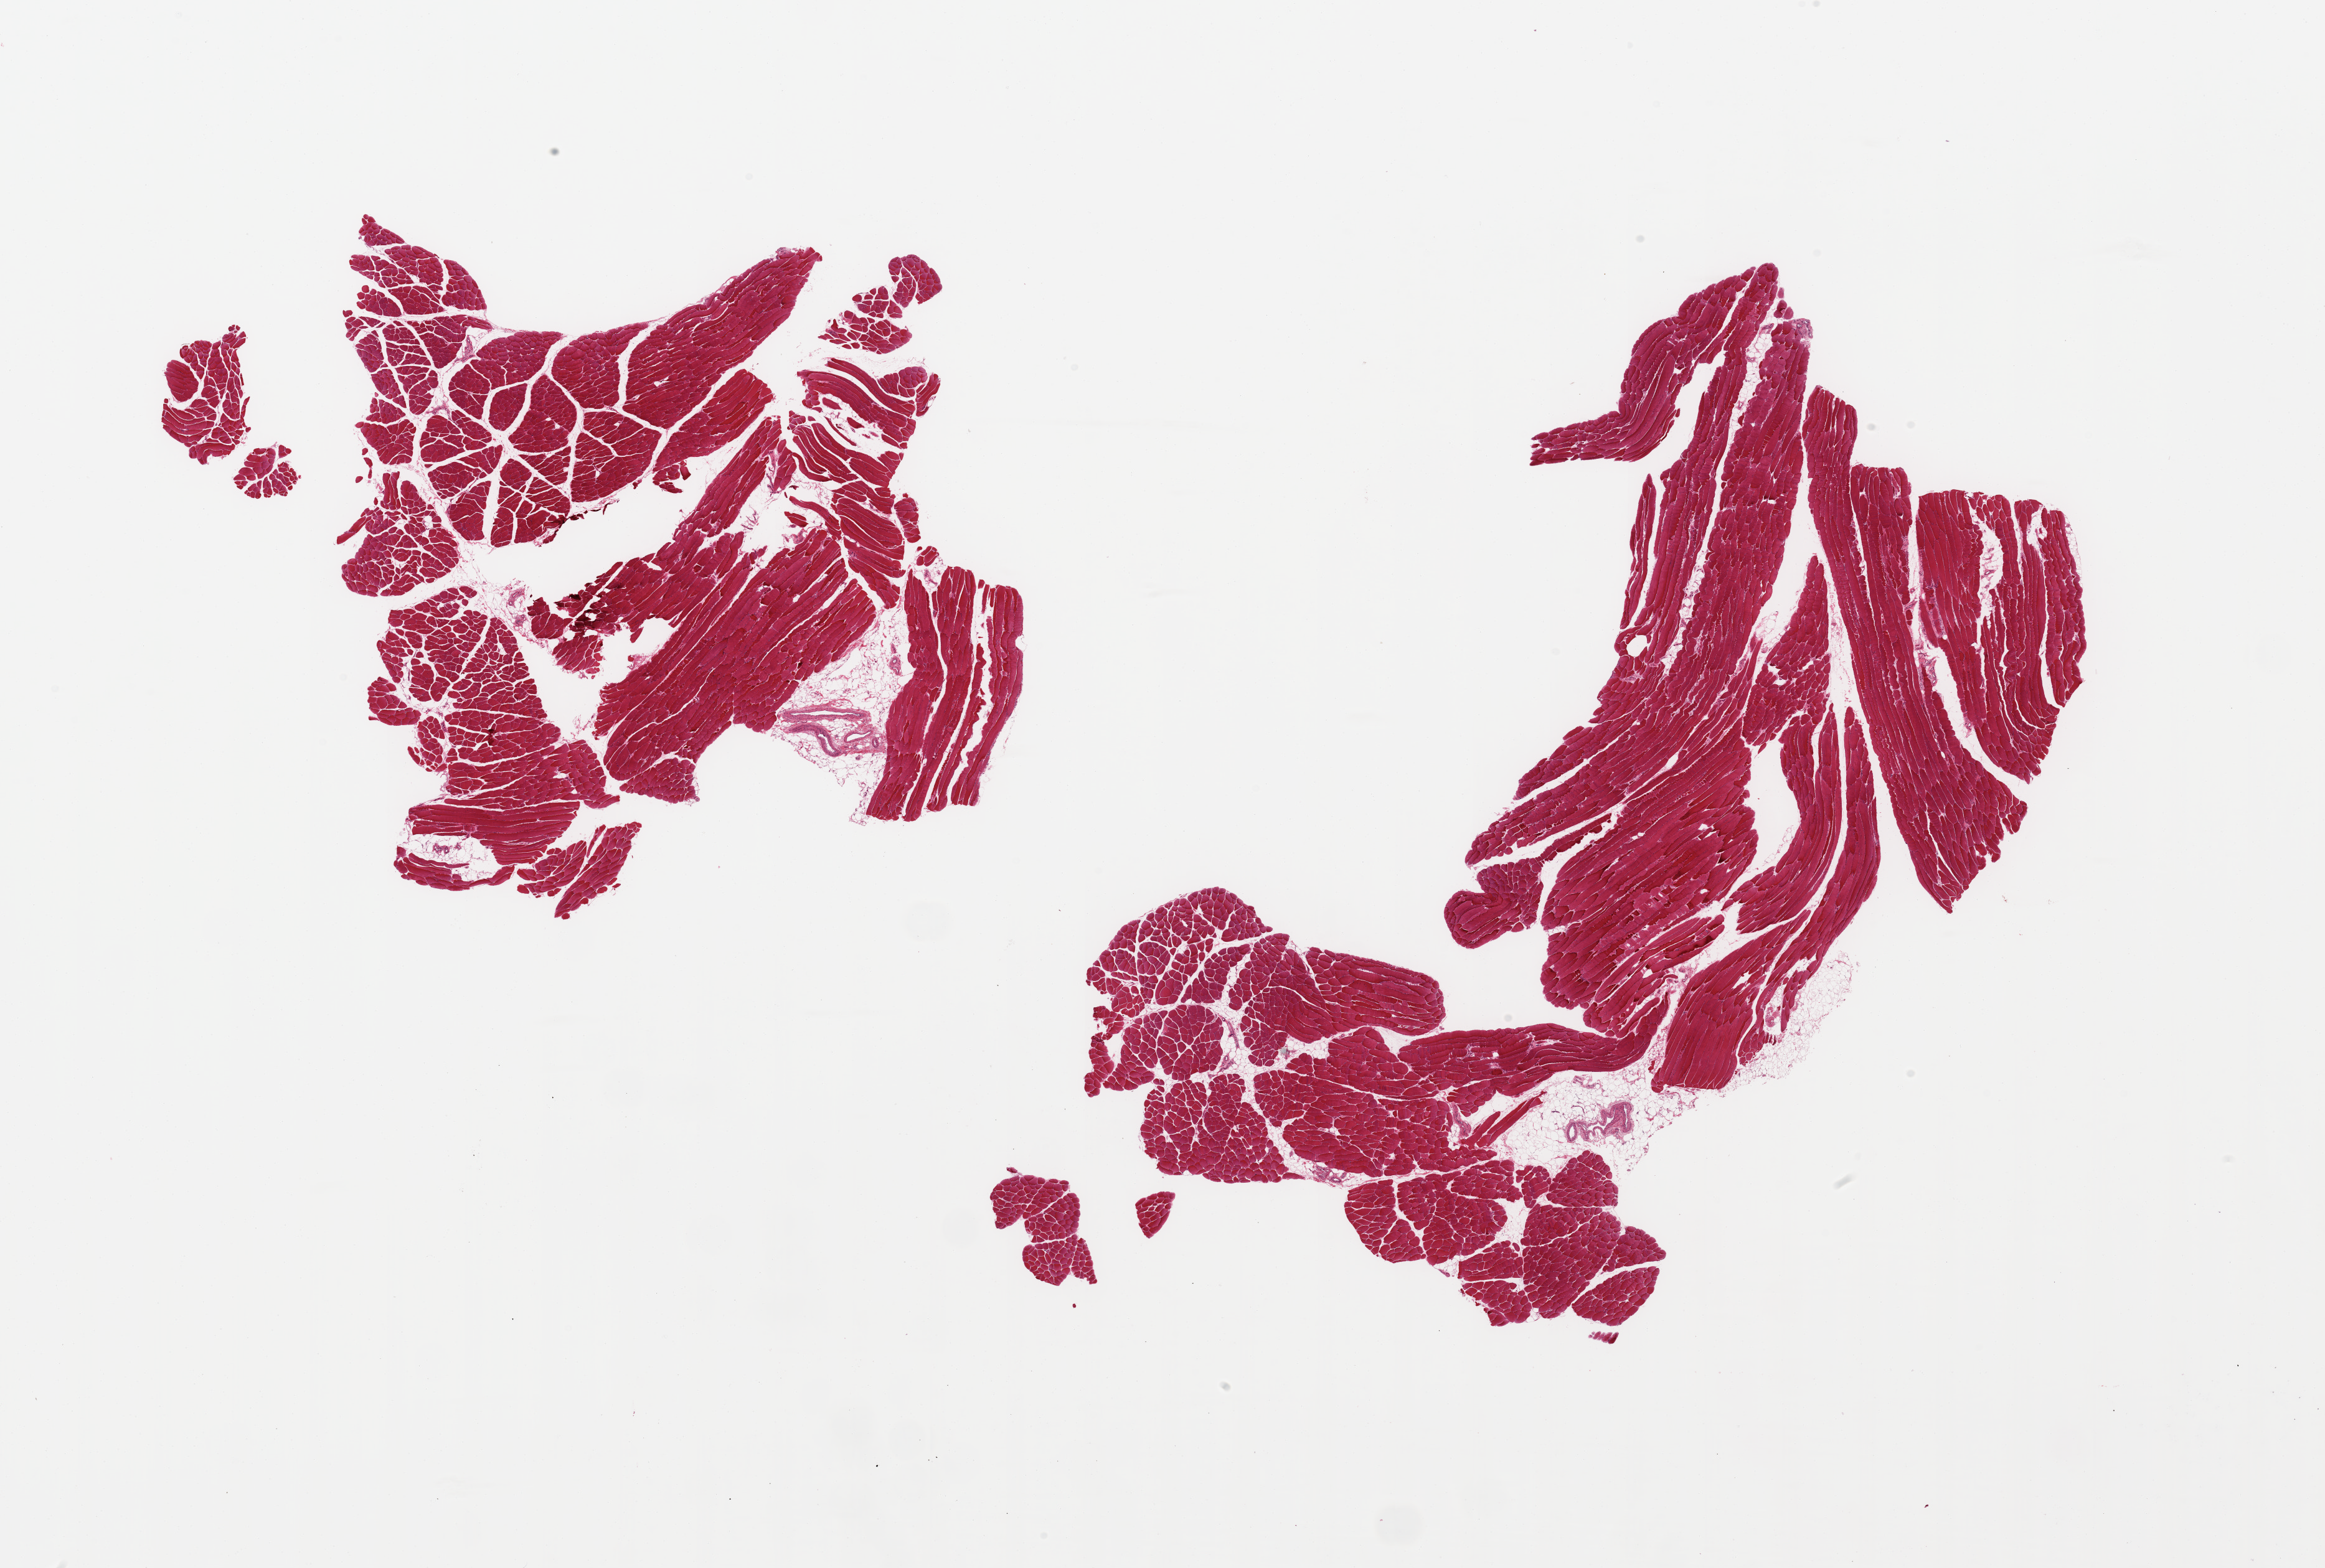
Digitized hematoxylin and eosin (H&E)-stained section, brightfield — low-resolution overview of the scanned area, about 29.5 x 19.9 mm, PAXgene-fixed paraffin-embedded (PFPE) section, target tissue: skeletal muscle, tissue donor sample. Male donor.
* pathologist's review note for this sample: 2 fragmented pieces; no lesions; <10% internal fat